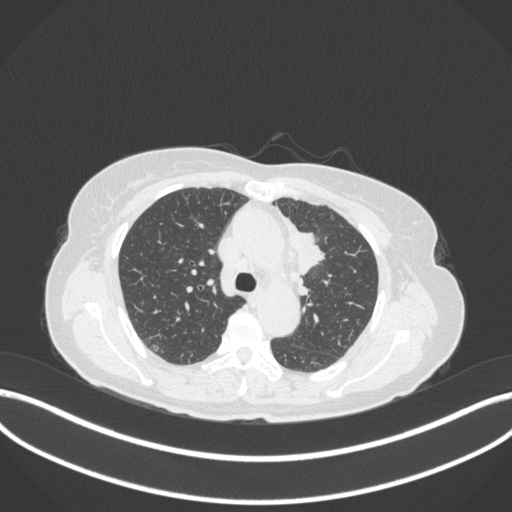
Chest CT, one axial slice; slice 232 of 368 in the series (ordered by position); 120 kVp; lung window (W 1500 / L -600 HU); 1 mm slice thickness; 512 × 512 image matrix. Female patient, age 65 years. From the clinical record (not read from this slice): clinical TNM (as recorded): T2a N0 M0; histopathological grade: G2-3.
Outlined on this slice (bounding box drawn by a radiologist):
- lung tumour (recorded histology: adenocarcinoma): bounding box (x1, y1, x2, y2) in pixels: (282, 216, 327, 278)